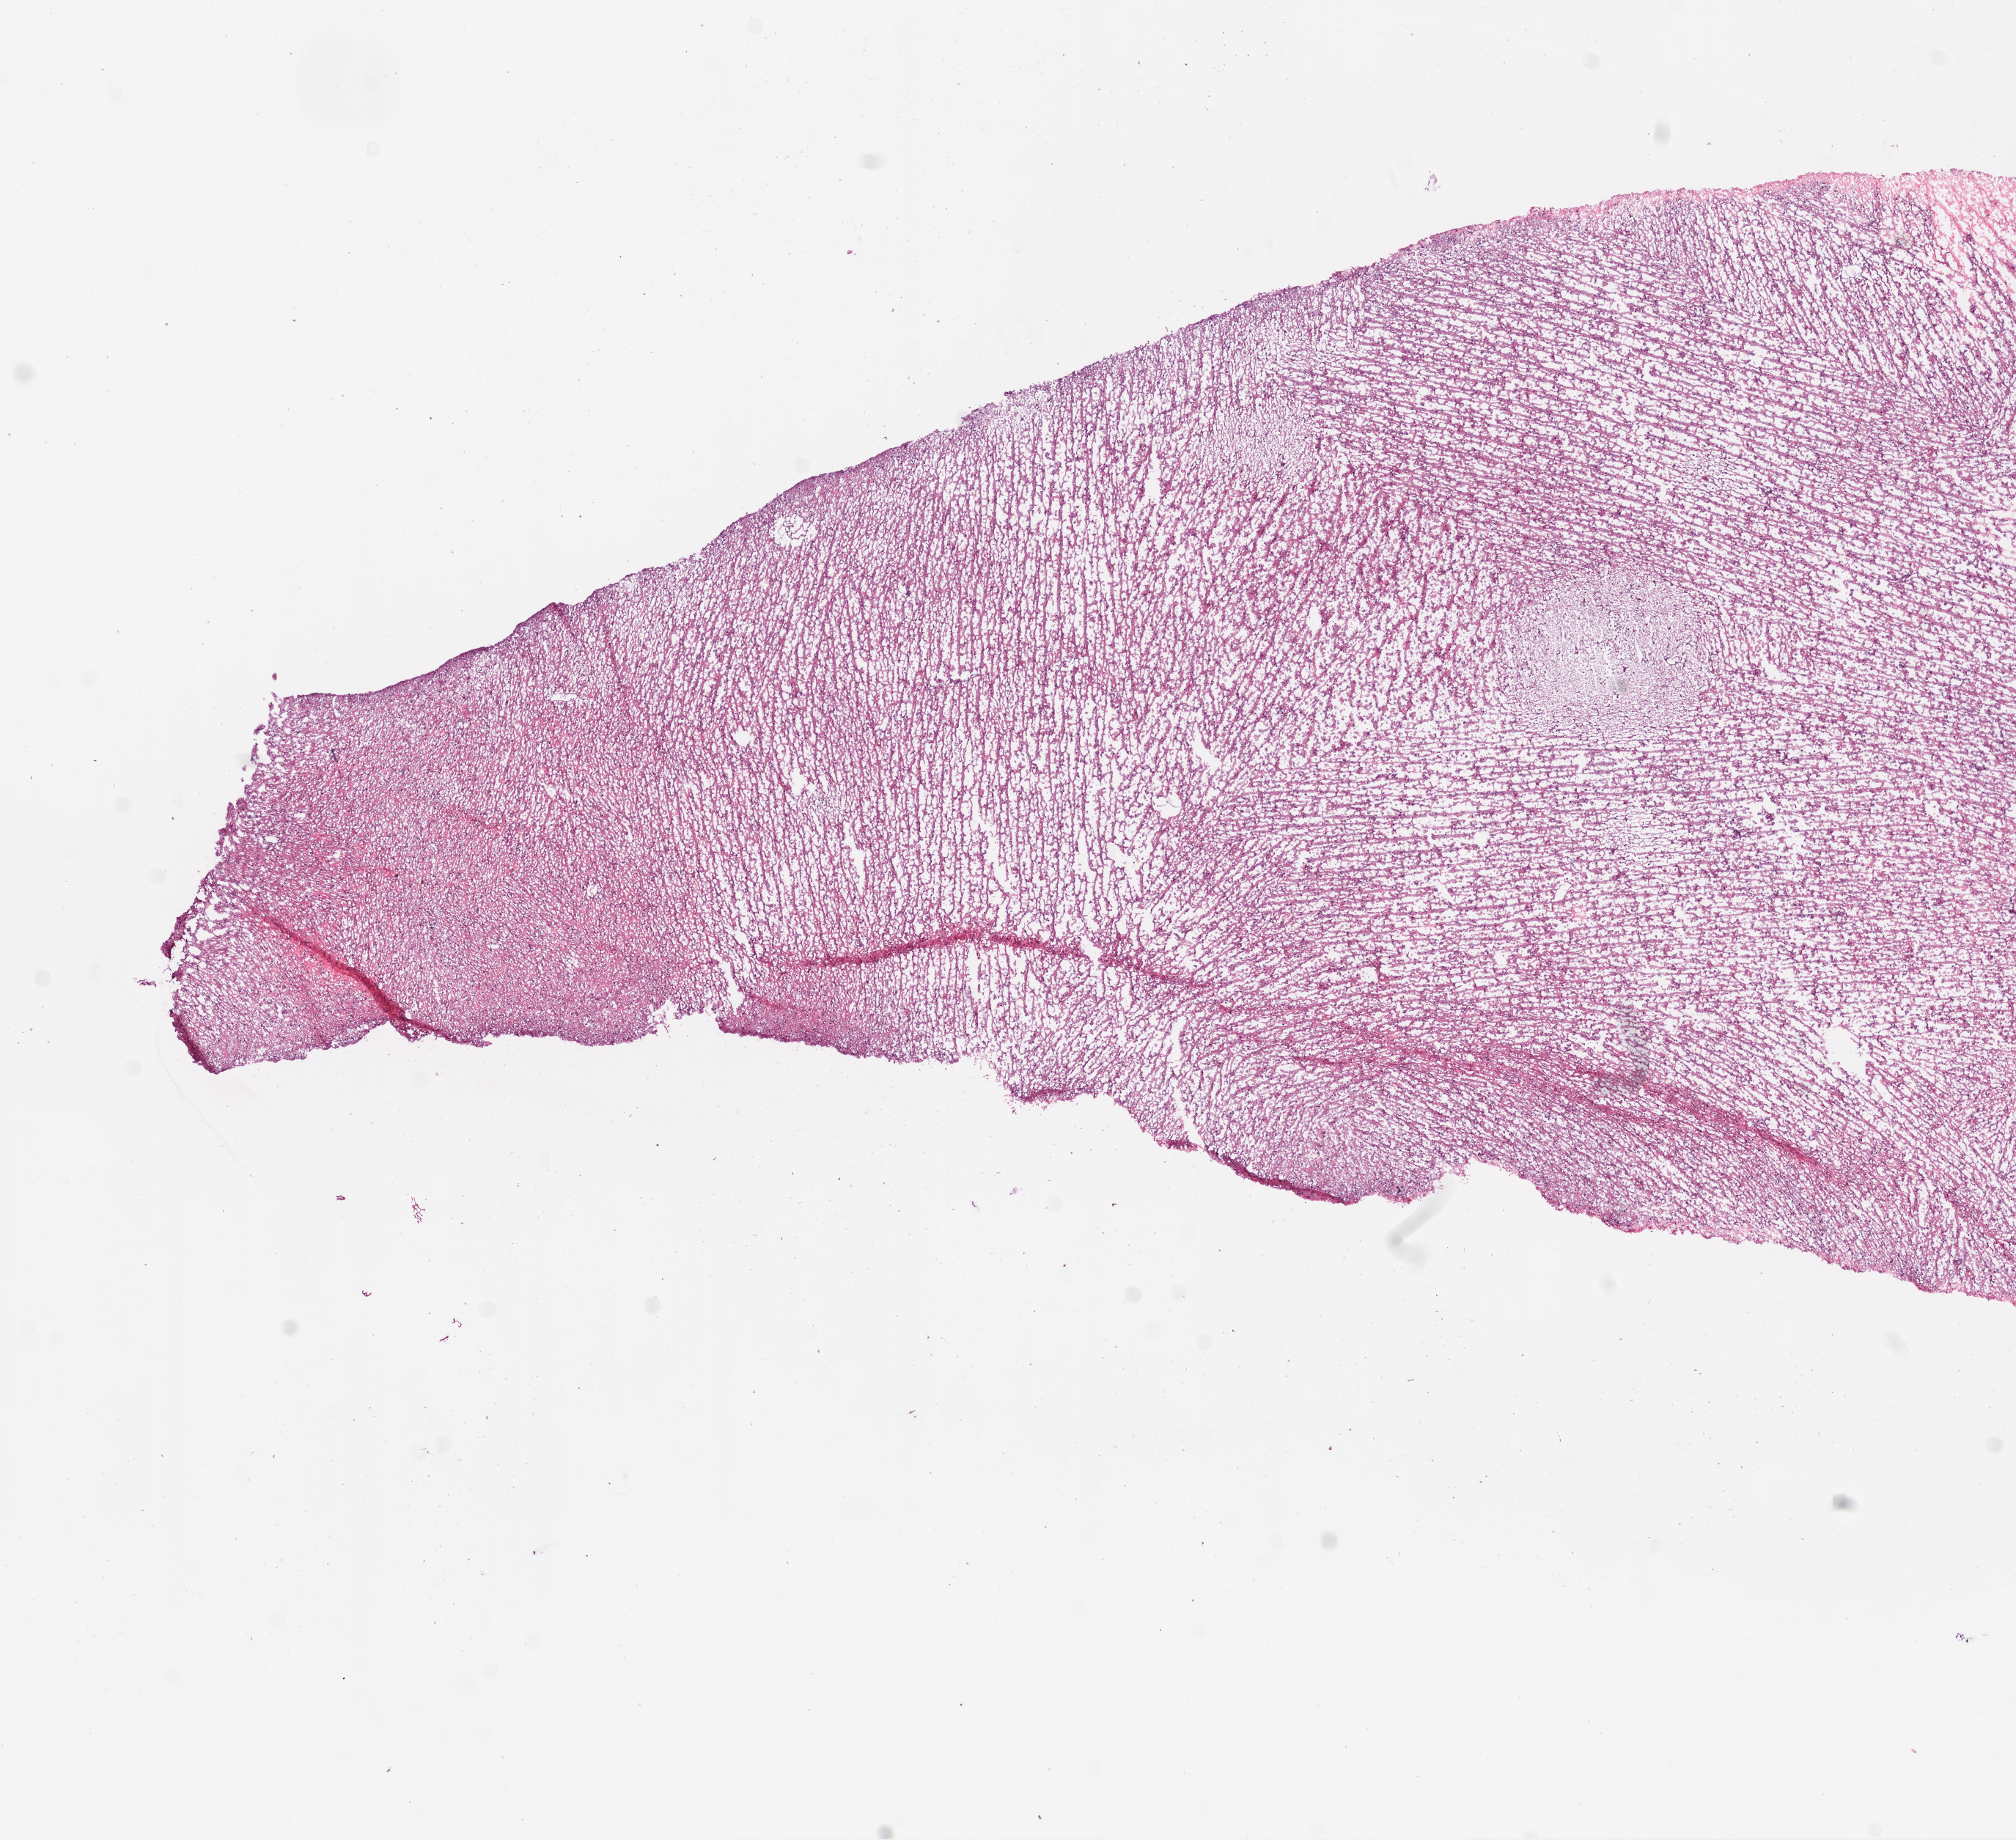
Digitized H&E tissue section (whole slide), a low-resolution overview of the entire scanned area, about 11.0 x 10.1 mm (from a 20x scan); frozen section; primary tumour sample from the brain. Patient: male, age at initial diagnosis 77 years.
Diagnosis: Glioblastoma.